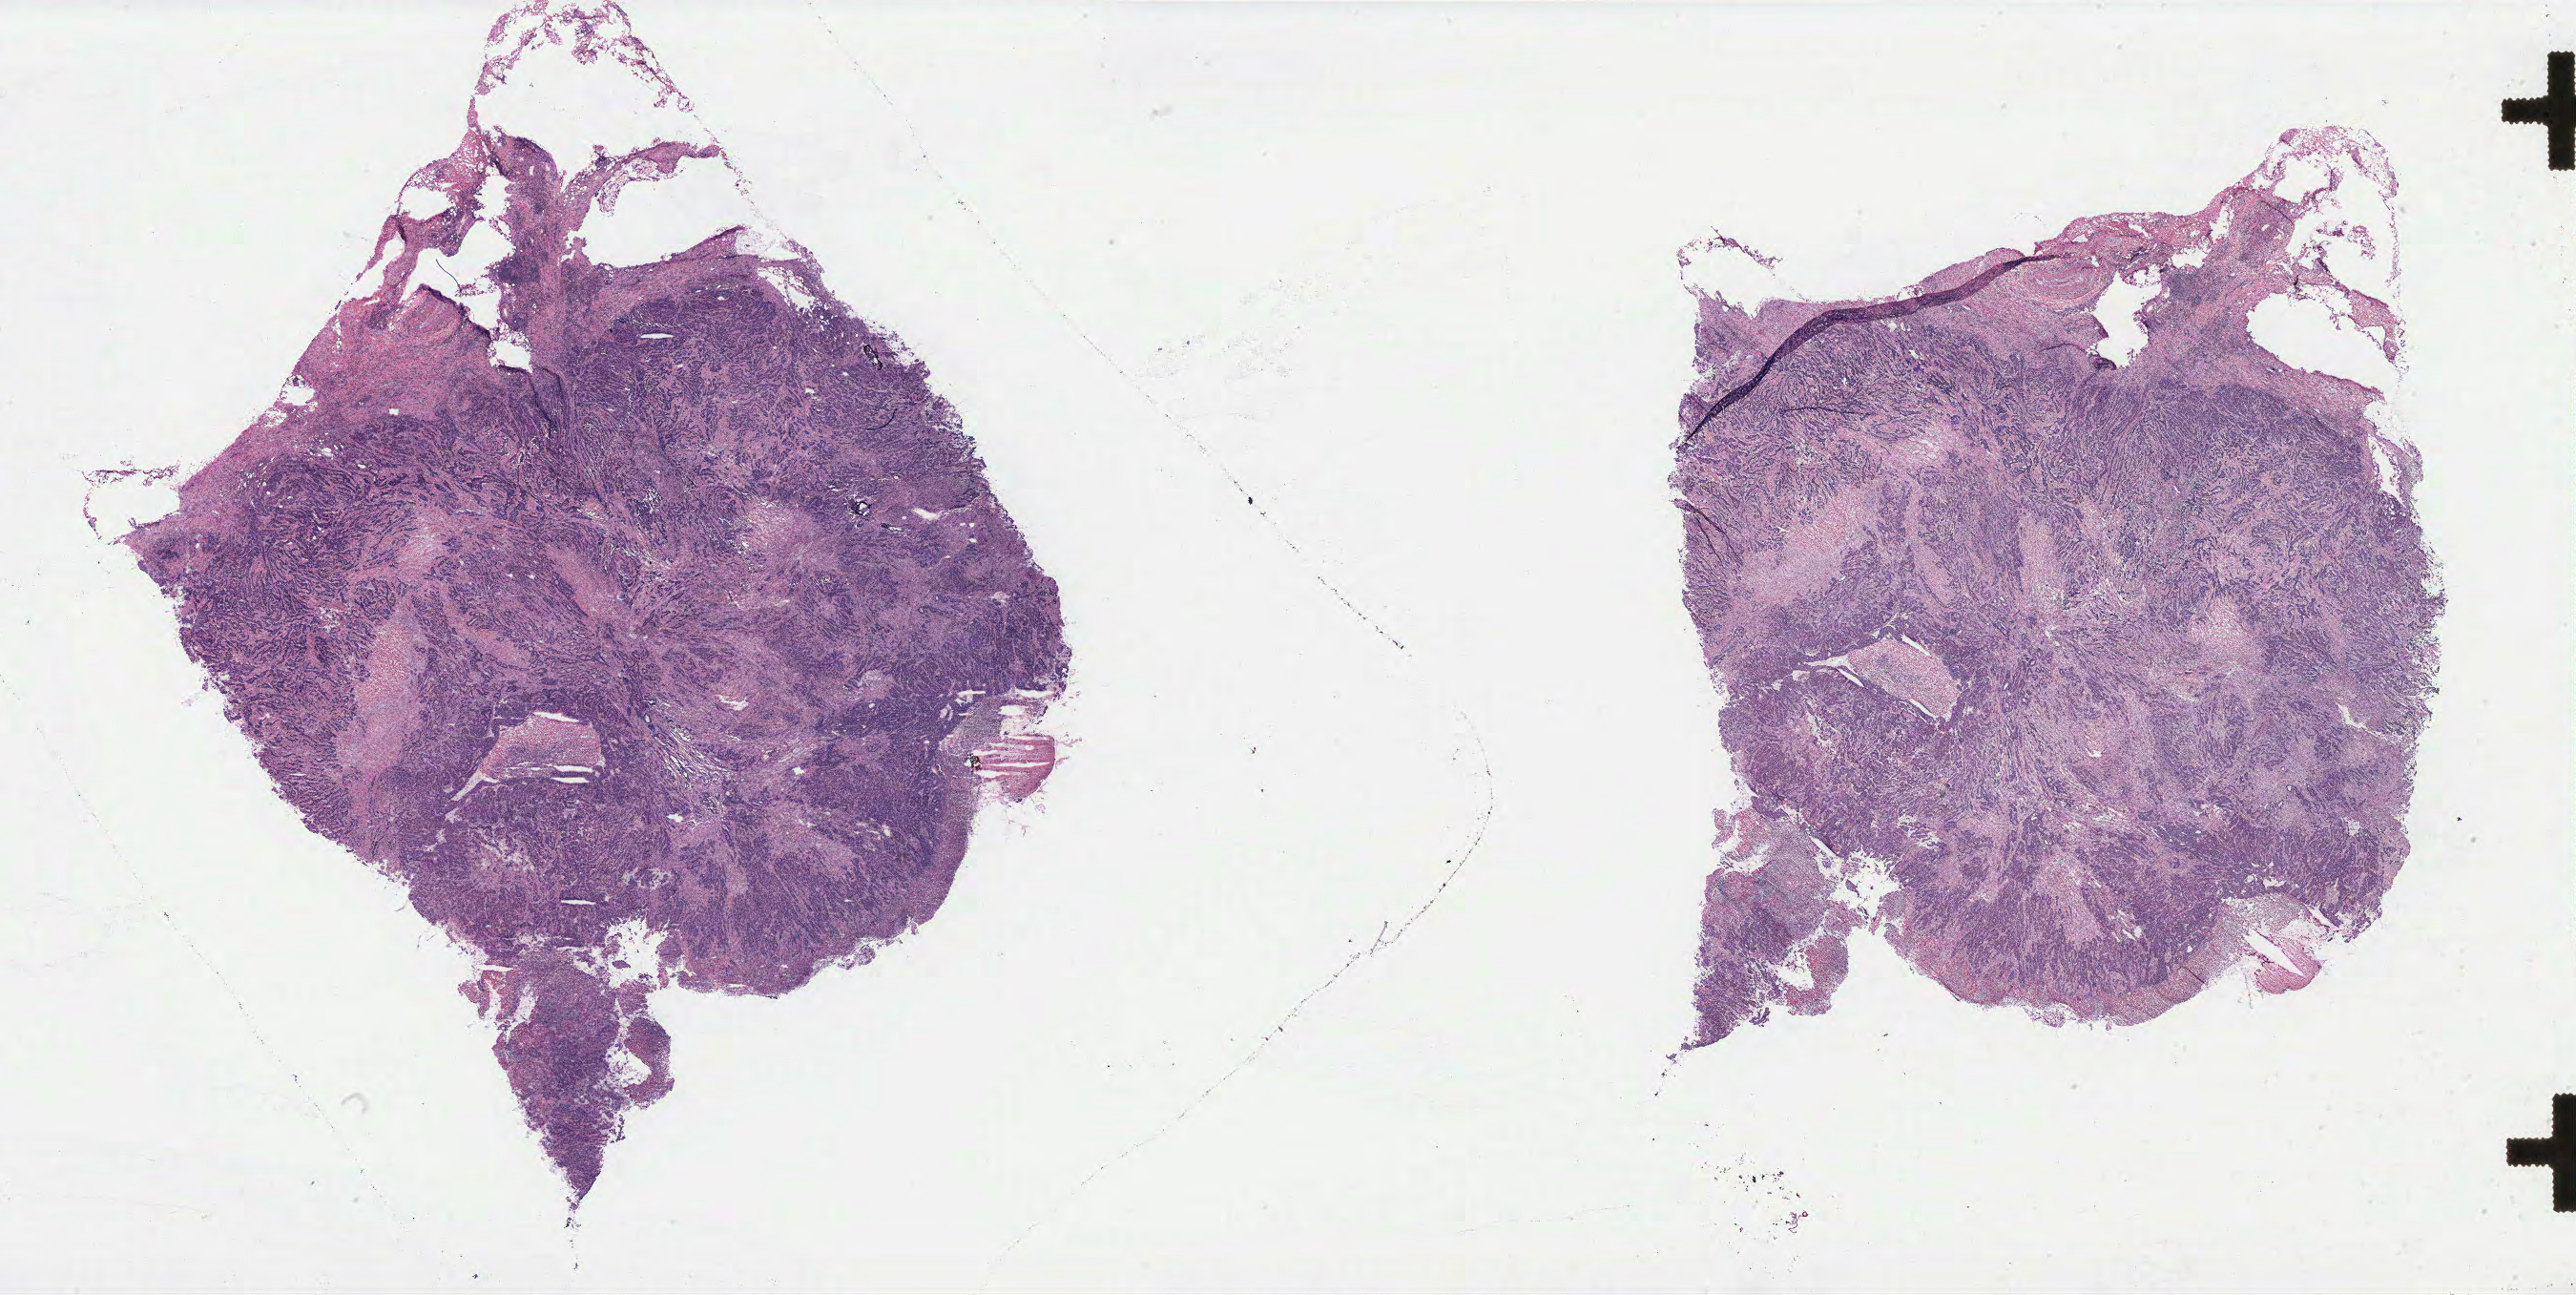
Digitized H&E-stained tissue section (whole slide), whole scanned area (about 43.2 x 21.7 mm, slide scanned at 40x) shown as a low-resolution overview; colon, tumour tissue. Patient: male, age 74 years.
Histologic diagnosis: Adenocarcinoma, NOS.